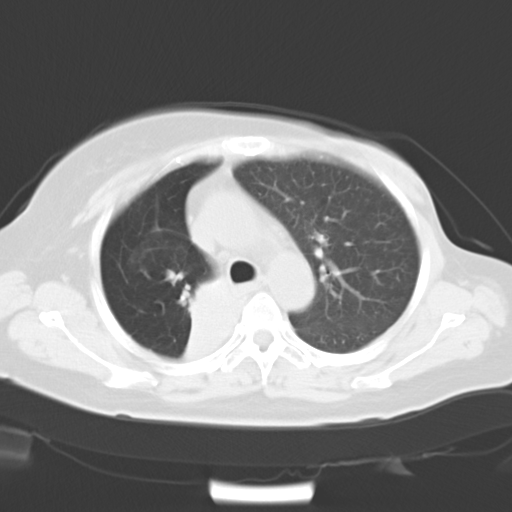
Chest CT, one axial slice. Slice 22 of 30 in the series (ordered by position). 120 kVp. Lung window (W 1500 / L -600 HU). 8 mm slice thickness. 512 × 512 image matrix. Female patient, age 53 years. From the clinical record (not read from this slice): clinical TNM (as recorded): T2b N1 M0.
Outlined on this slice (rectangle marked by the reading radiologist):
- lung tumour (recorded histology: adenocarcinoma): bounding box [x1, y1, x2, y2] px = [172, 275, 232, 348]